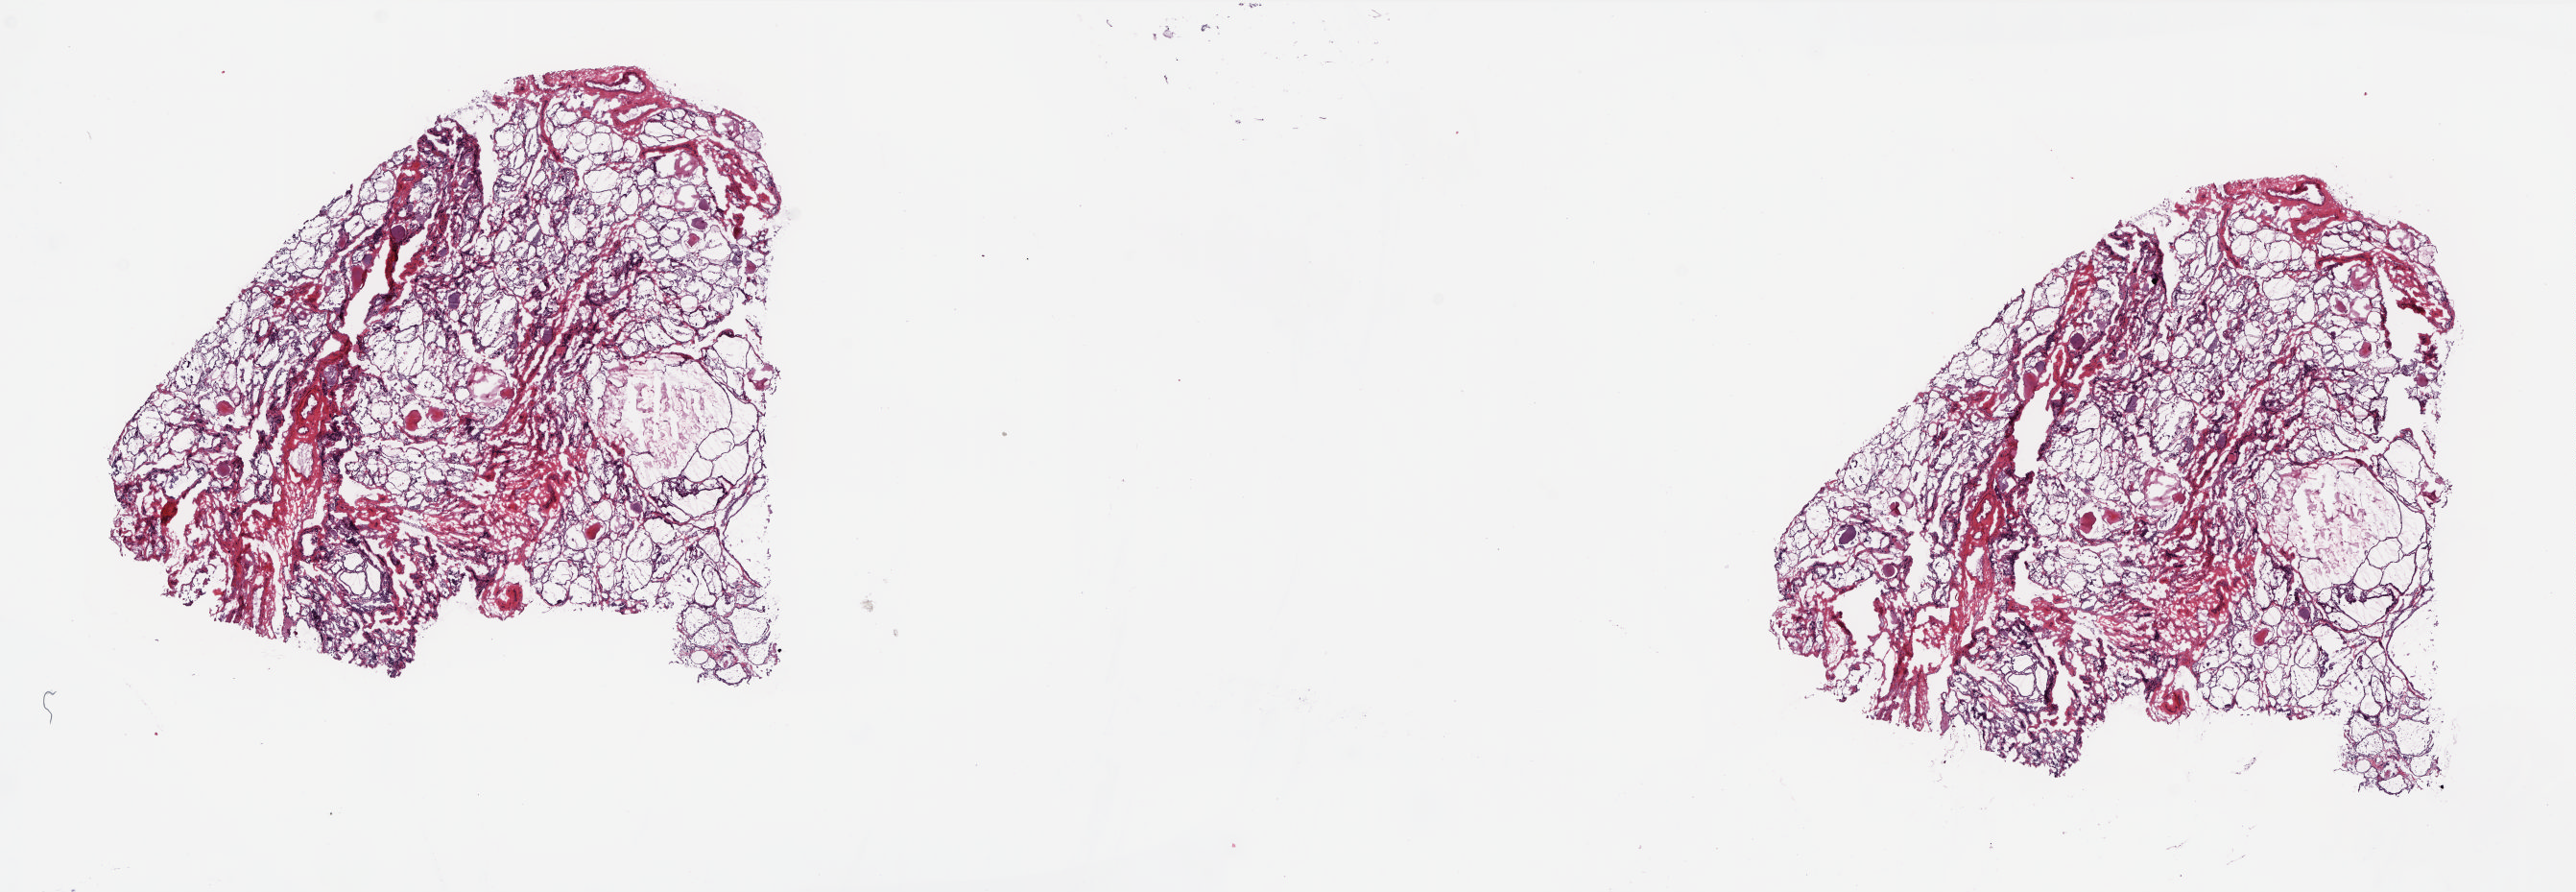
Digitized H&E tissue section (whole slide) — shown as a low-resolution overview of the whole scanned area (about 21.6 x 7.5 mm), frozen section from the top of the tissue portion, thyroid, solid tissue normal (non-tumour tissue) sample. Patient: female, age at initial diagnosis 68 years. Slide review estimates, as recorded: tumour cells 0%, tumour nuclei 0%, normal cells 70%, stromal cells 30%, necrosis 0%. Inflammatory infiltration, as recorded: lymphocyte infiltration 3%, monocyte infiltration 3%, neutrophil infiltration 0%.
- this section: solid tissue normal sample (biorepository sample class)
- patient diagnosis: Papillary adenocarcinoma, NOS (thyroid gland)